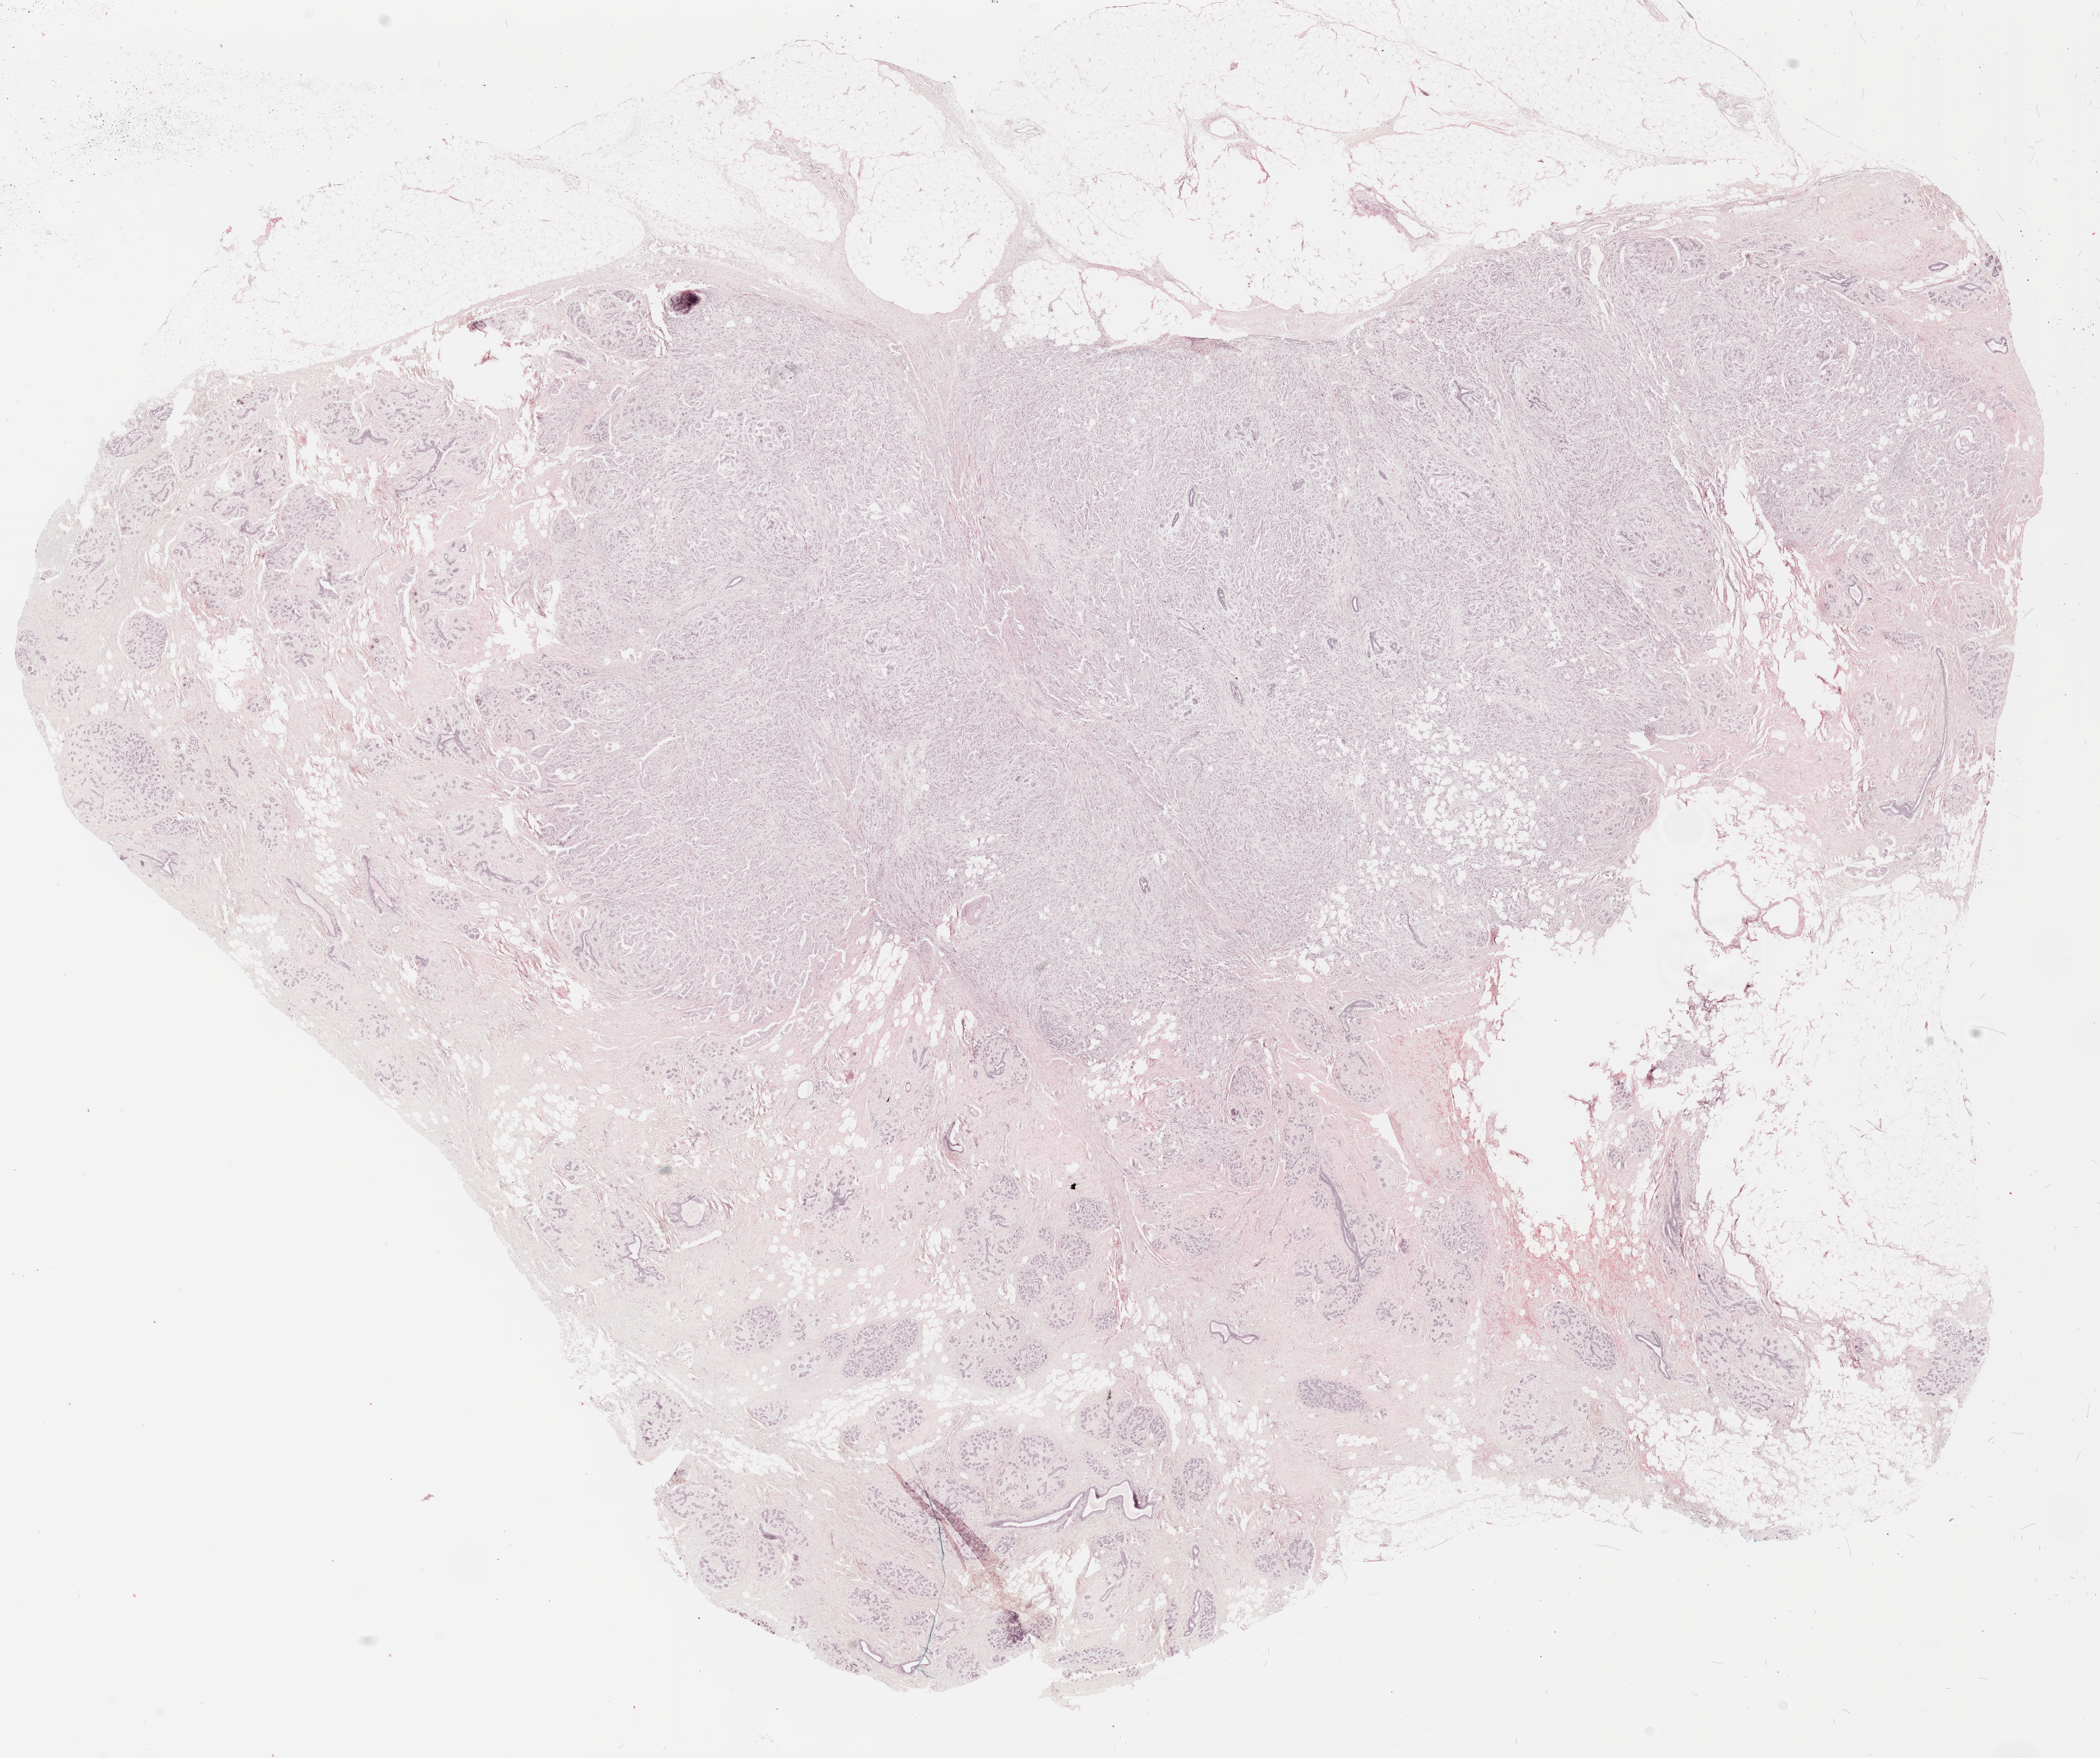
H&E whole-slide image — whole scanned area (about 24.9 x 20.8 mm) shown as a low-resolution overview, formalin-fixed paraffin-embedded (FFPE) diagnostic section, breast, primary tumour sample. Female patient; age at initial diagnosis 36 years.
Diagnosis: Infiltrating duct carcinoma, NOS.